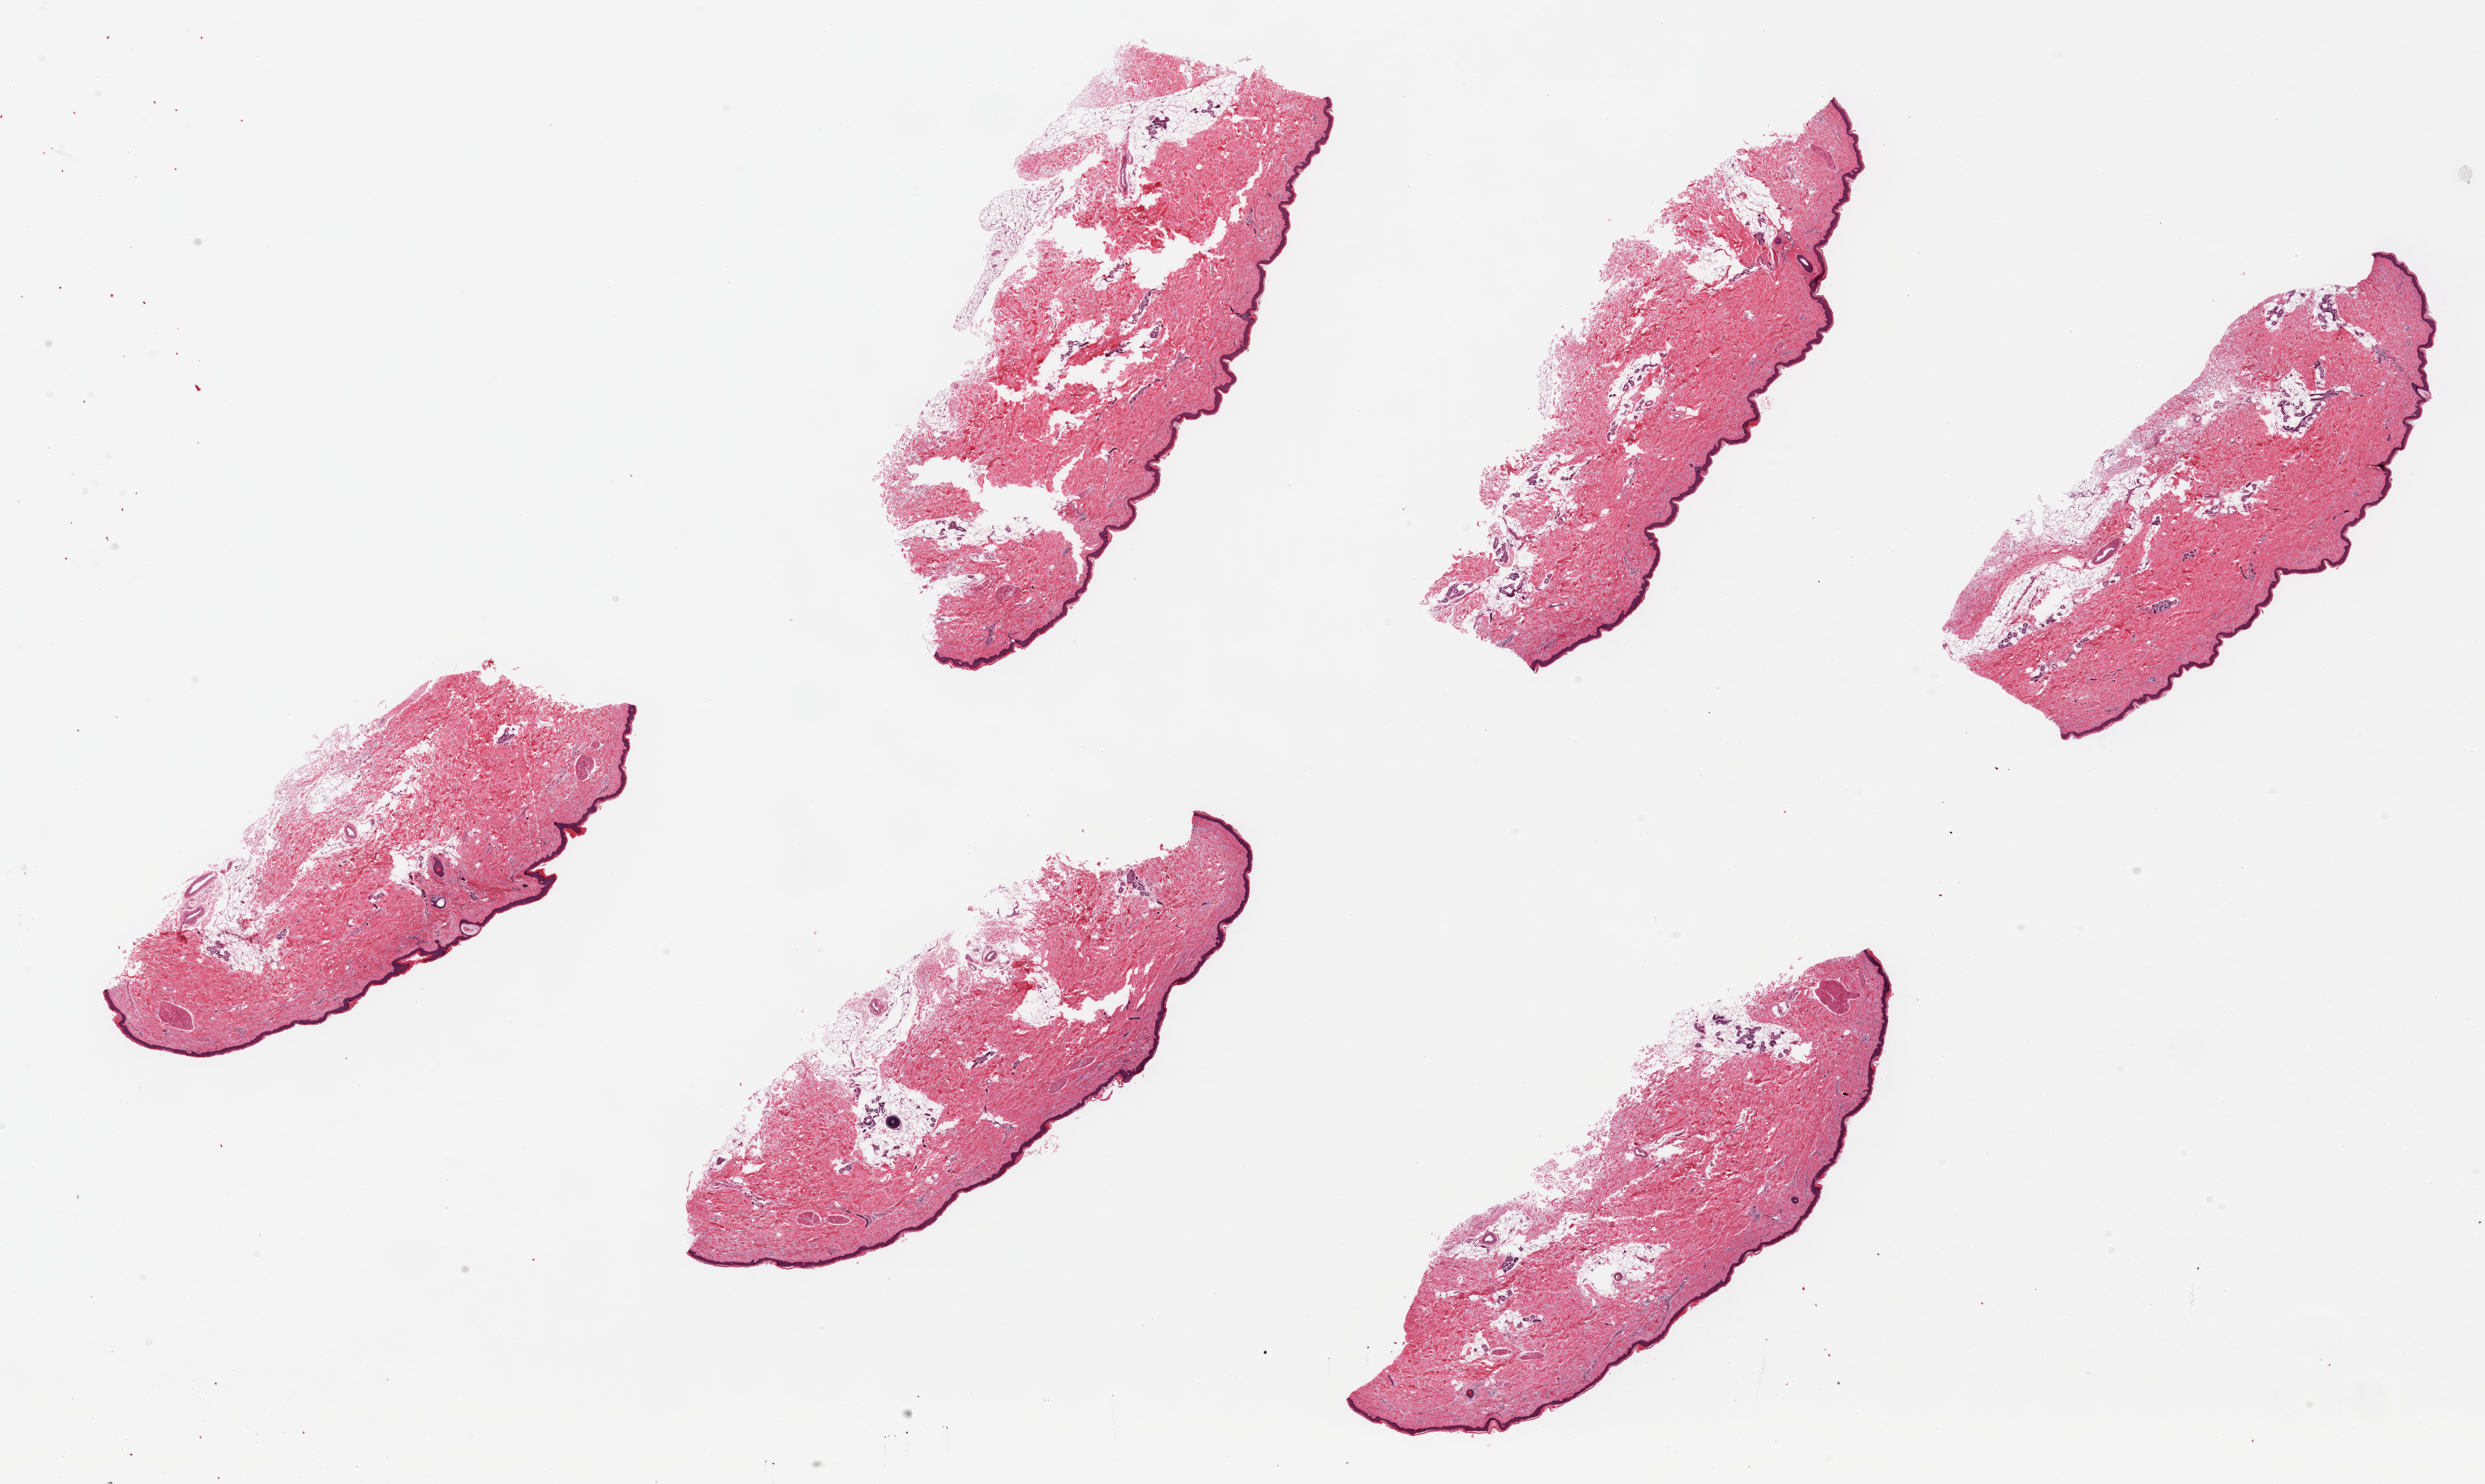
Haematoxylin and eosin whole-slide image, a low-resolution overview of the entire scanned area, about 29.5 x 17.6 mm (slide scanned at 20x), PAXgene-fixed paraffin-embedded (PFPE) section, section of skin of lower leg (target tissue), tissue donor sample. Female donor.
- pathologist's review note for this sample: 6 pieces up to 8x3 mm